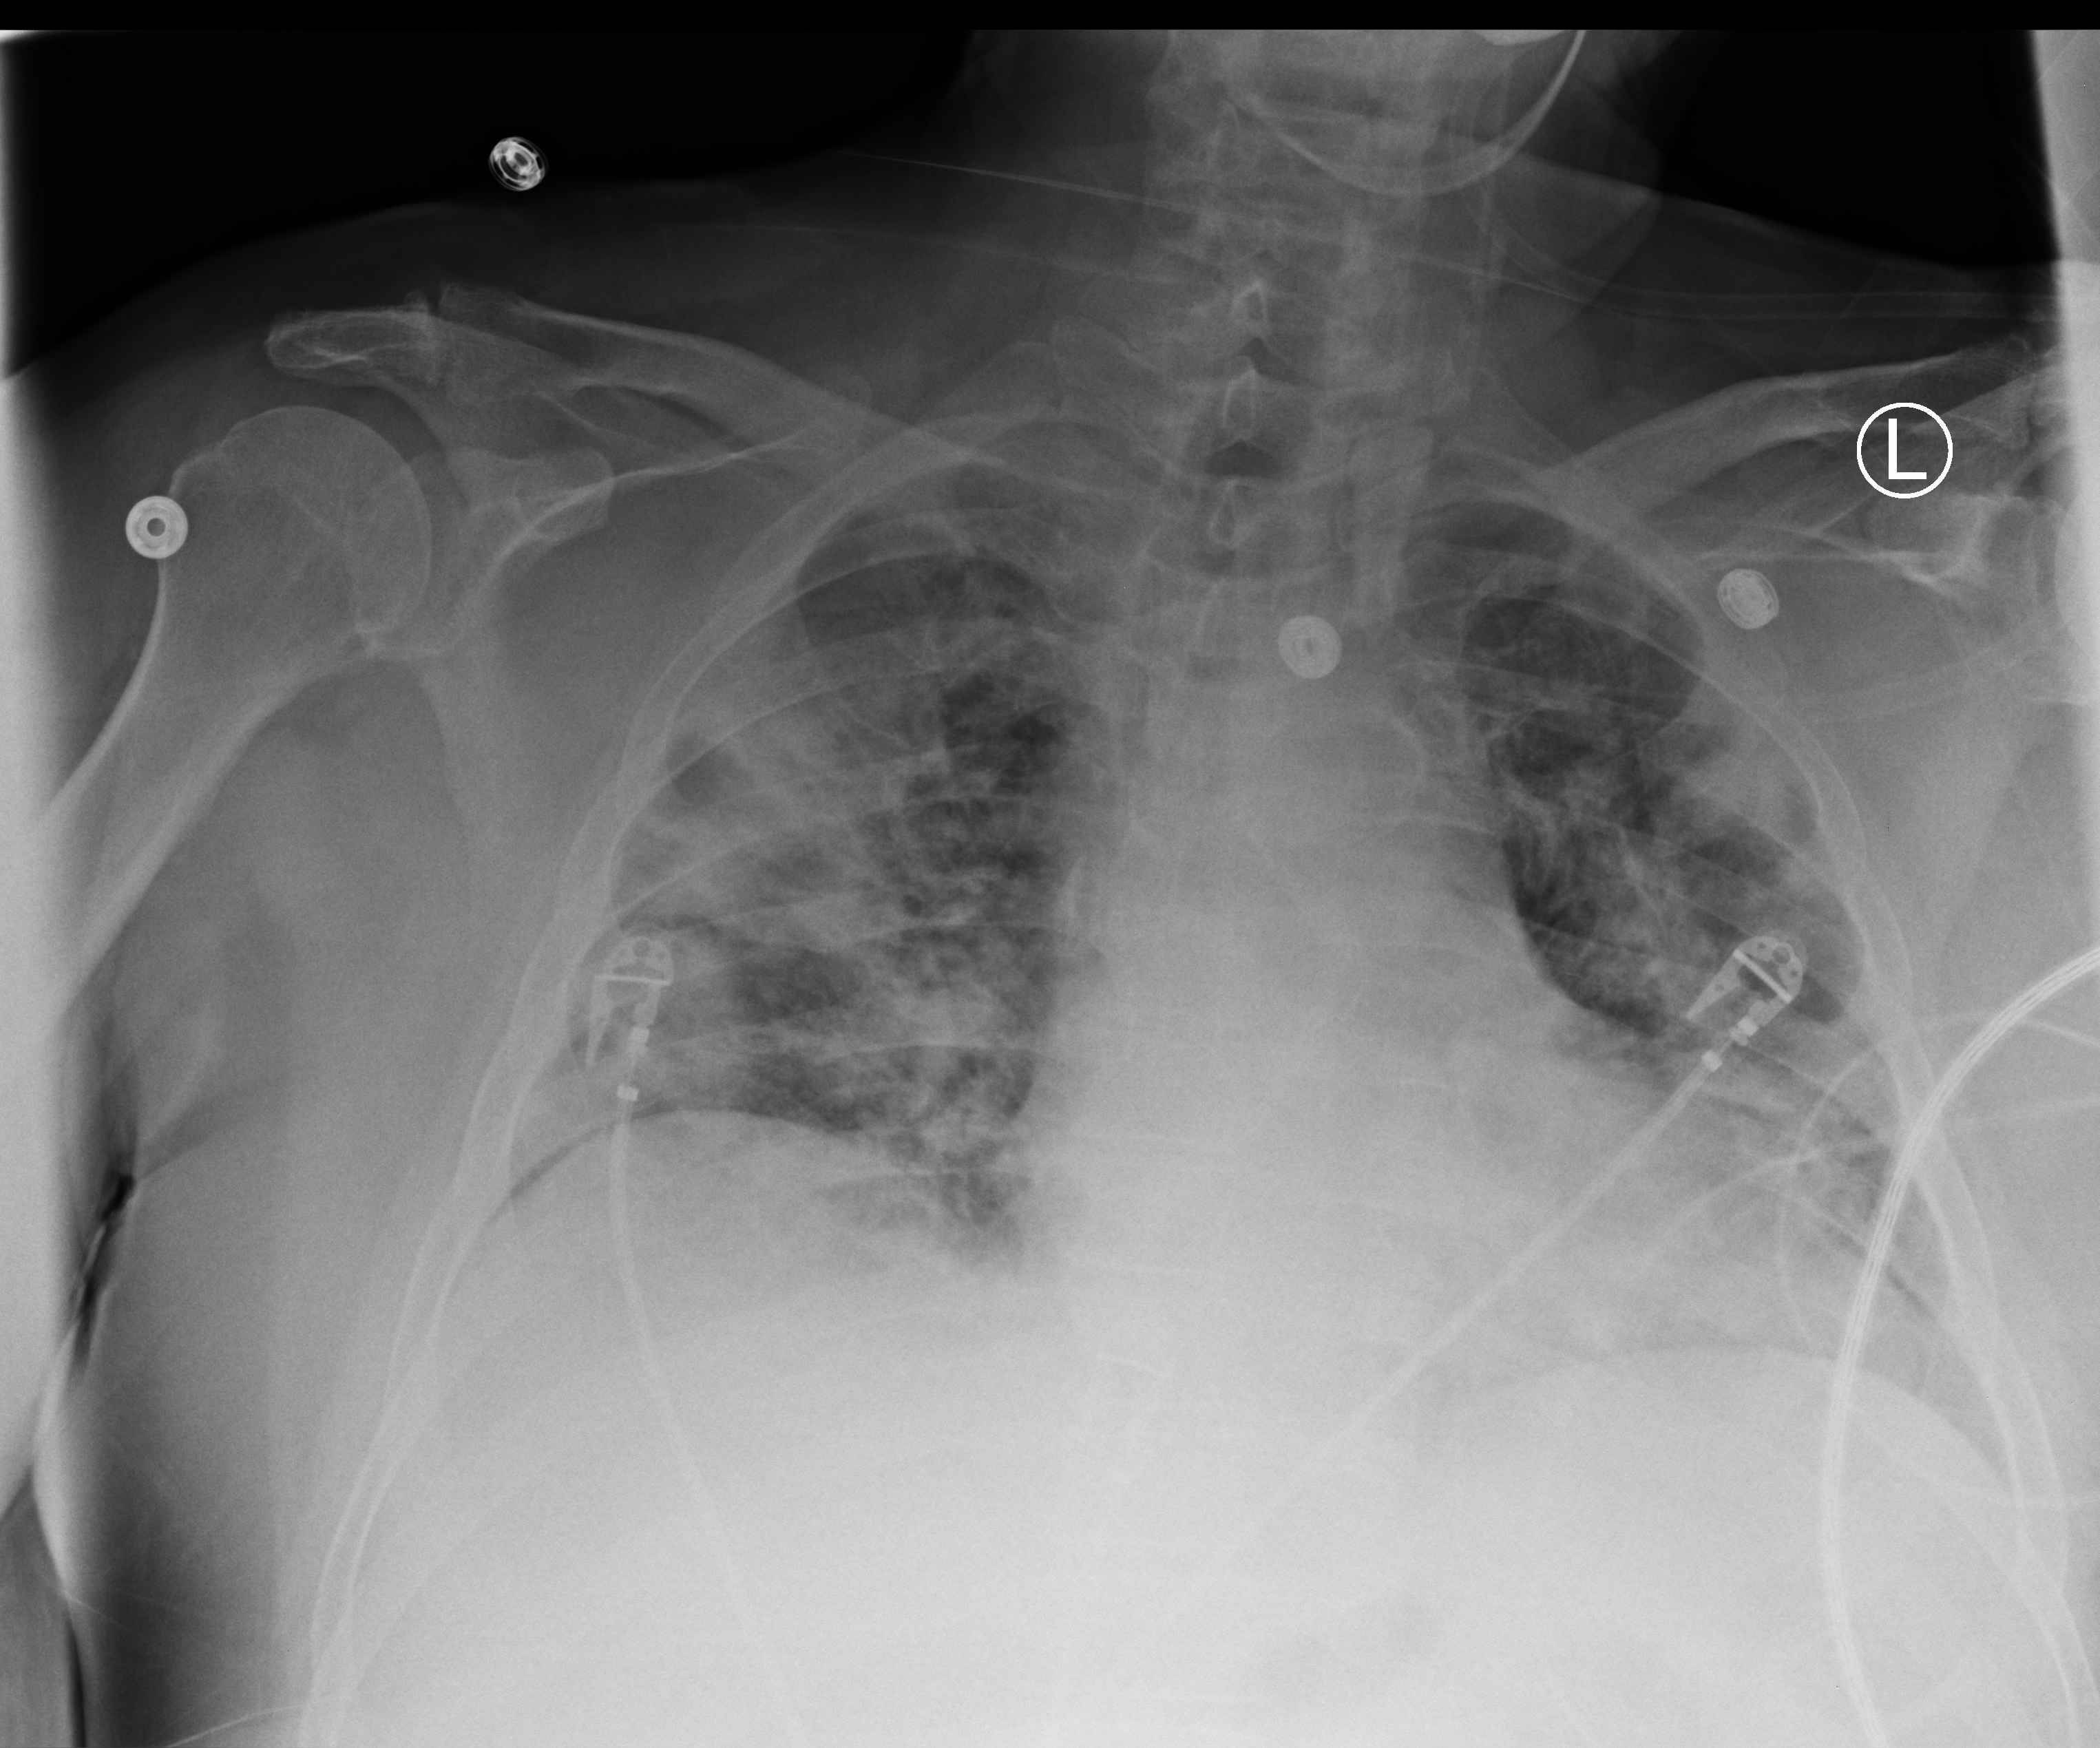
Chest X-ray (portable), anteroposterior (AP) projection. Patient hospitalised with COVID-19; male, aged 60–74 years.
Hospital-stay facts (about this admission, not read from this image; timing relative to this image not recorded):
- diabetes (admission record): yes